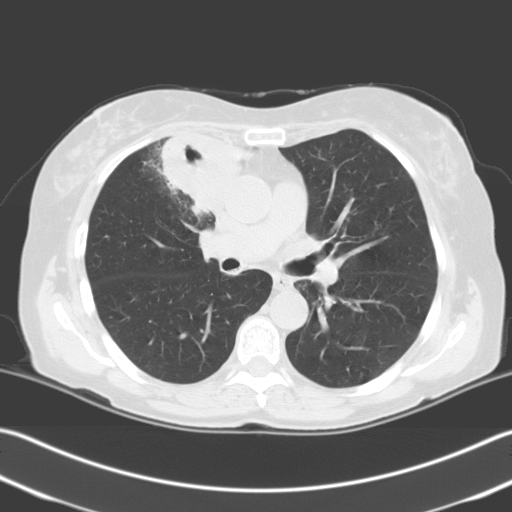
Low-dose screening chest CT, one axial slice; position 127 of 204 along the scan axis; lung window (W 1500 / L -600 HU); 512 × 512 image matrix.
Structures marked on this image (manually delineated by an expert):
- lesion 1 (tumor, upper lobe of right lung): bounding box (x1, y1, x2, y2) in pixels: (160, 132, 255, 216)